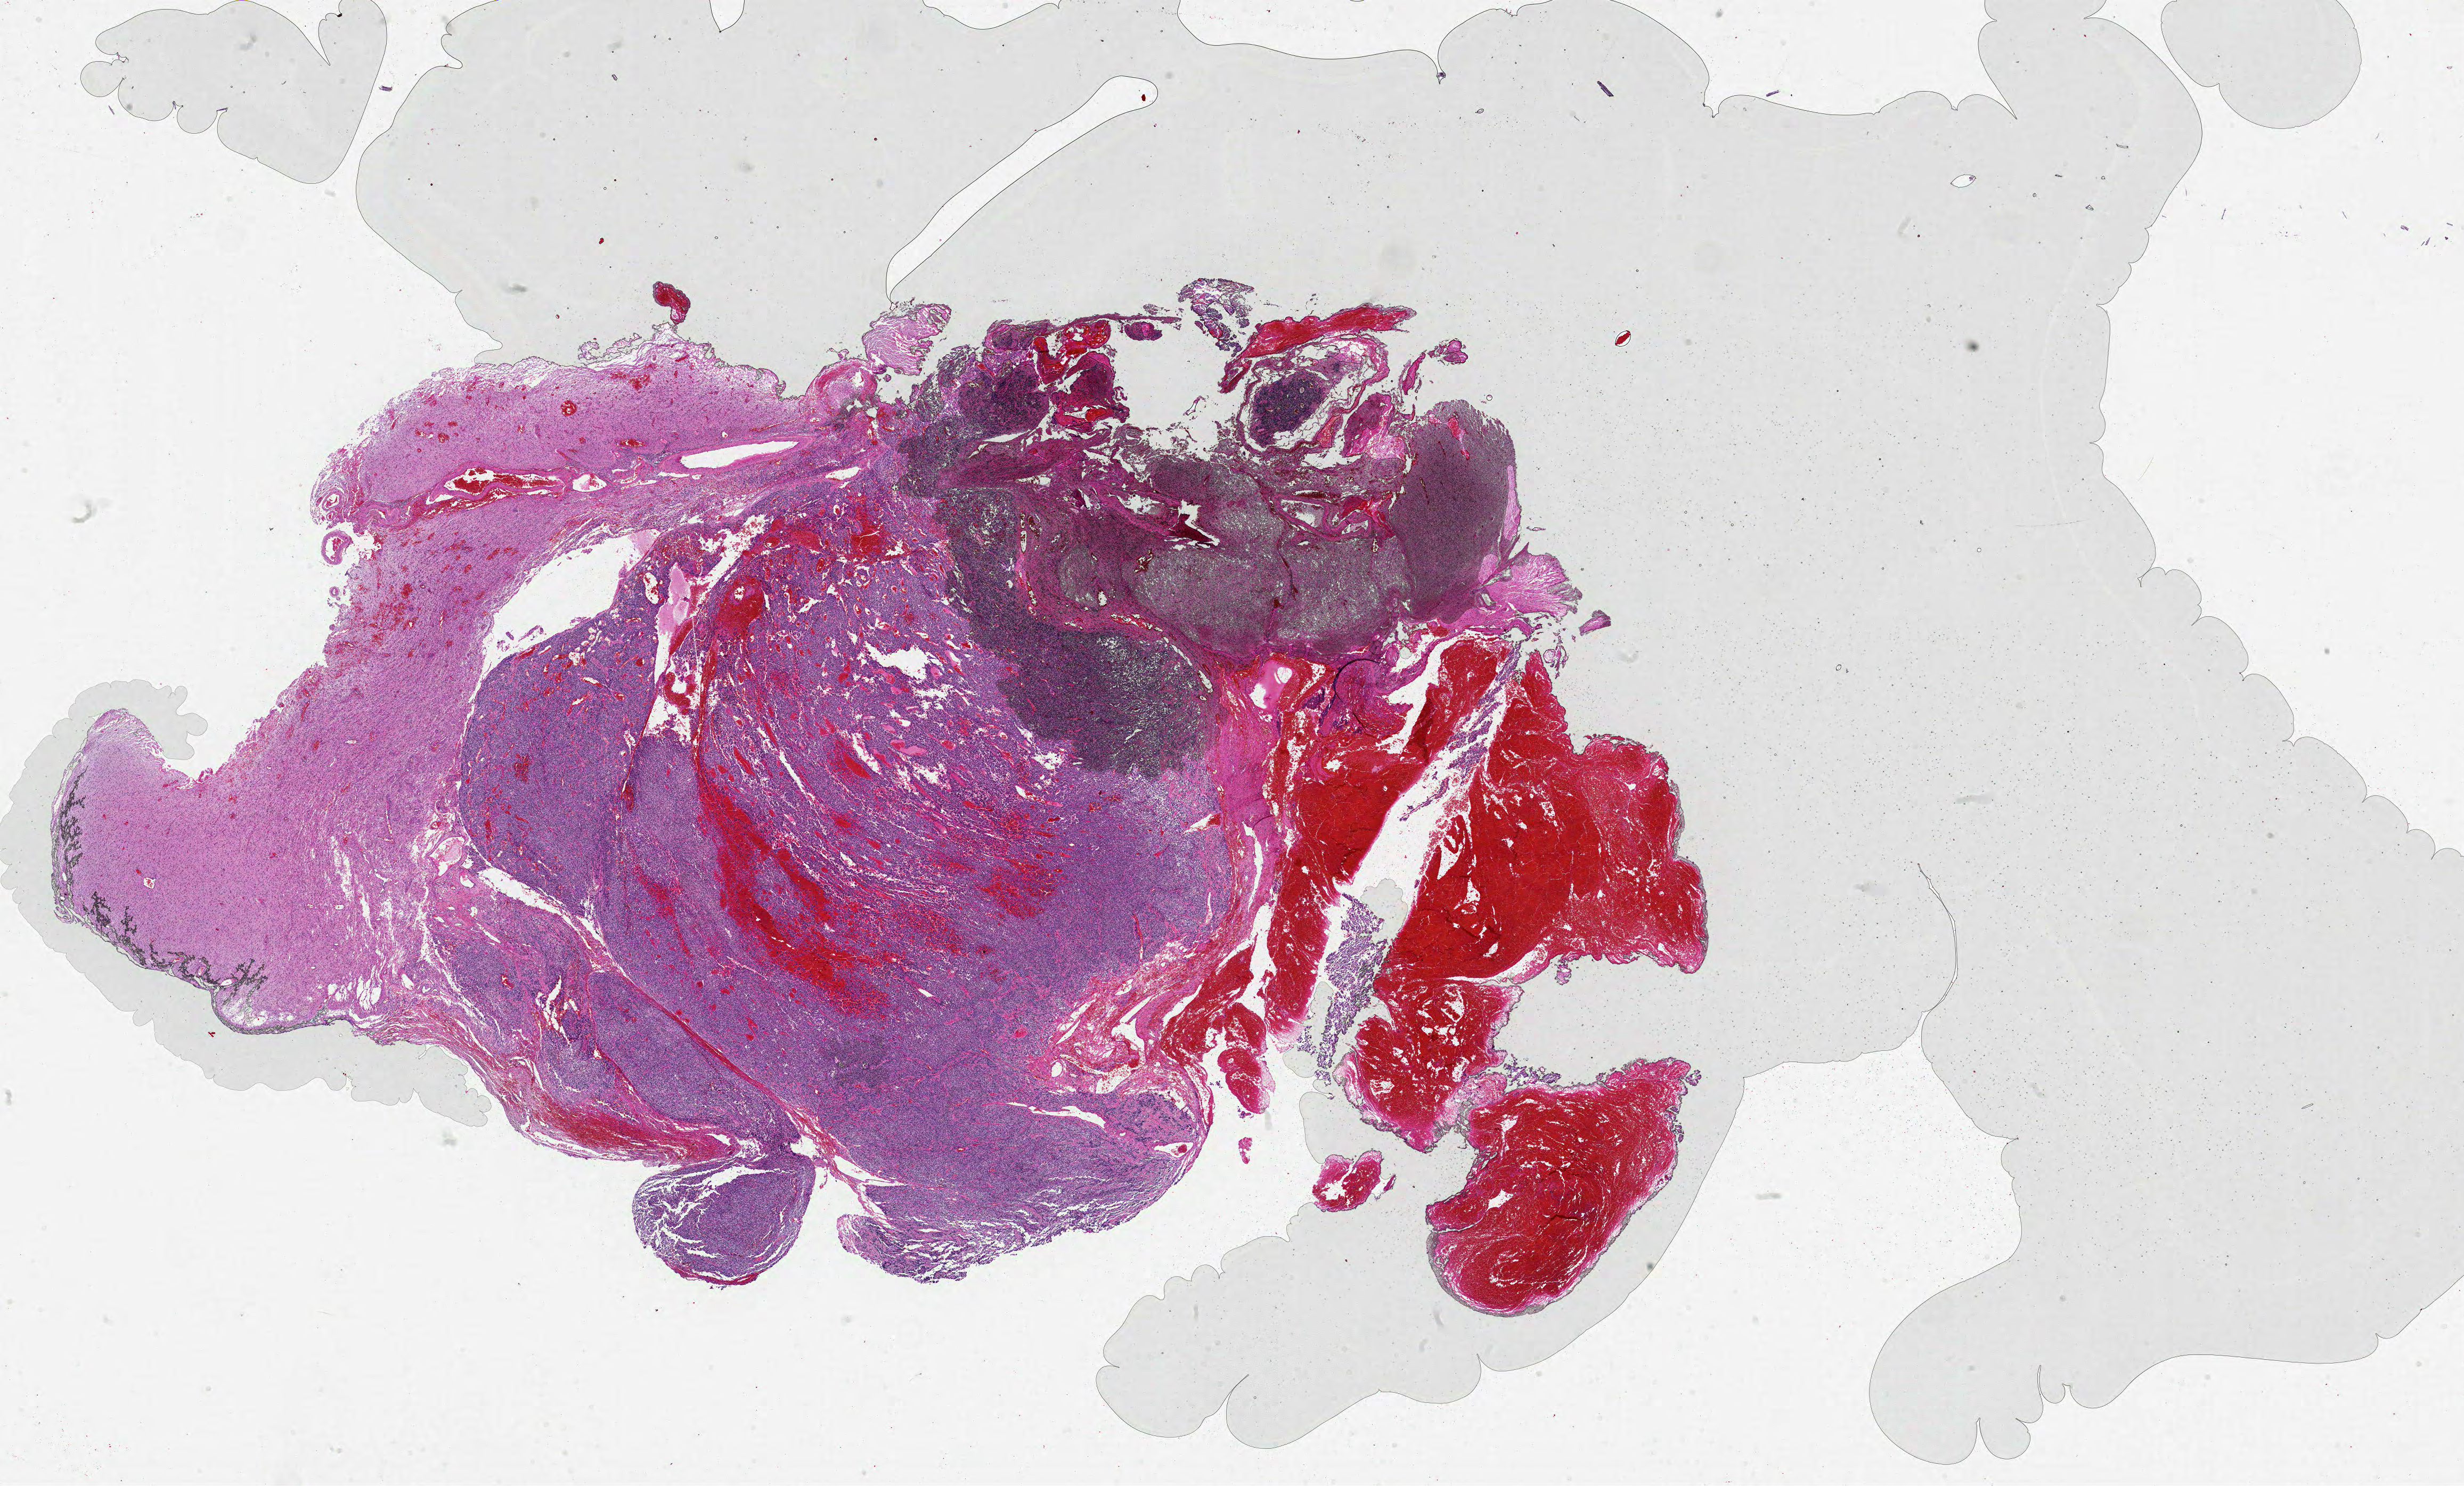
H&E-stained whole-slide image, low-resolution overview of the scanned area, about 37.0 x 22.3 mm; formalin-fixed paraffin-embedded (FFPE) diagnostic section; sample: primary tumour, brain. Patient: male, age at initial diagnosis 52 years.
Diagnosis: Glioblastoma.